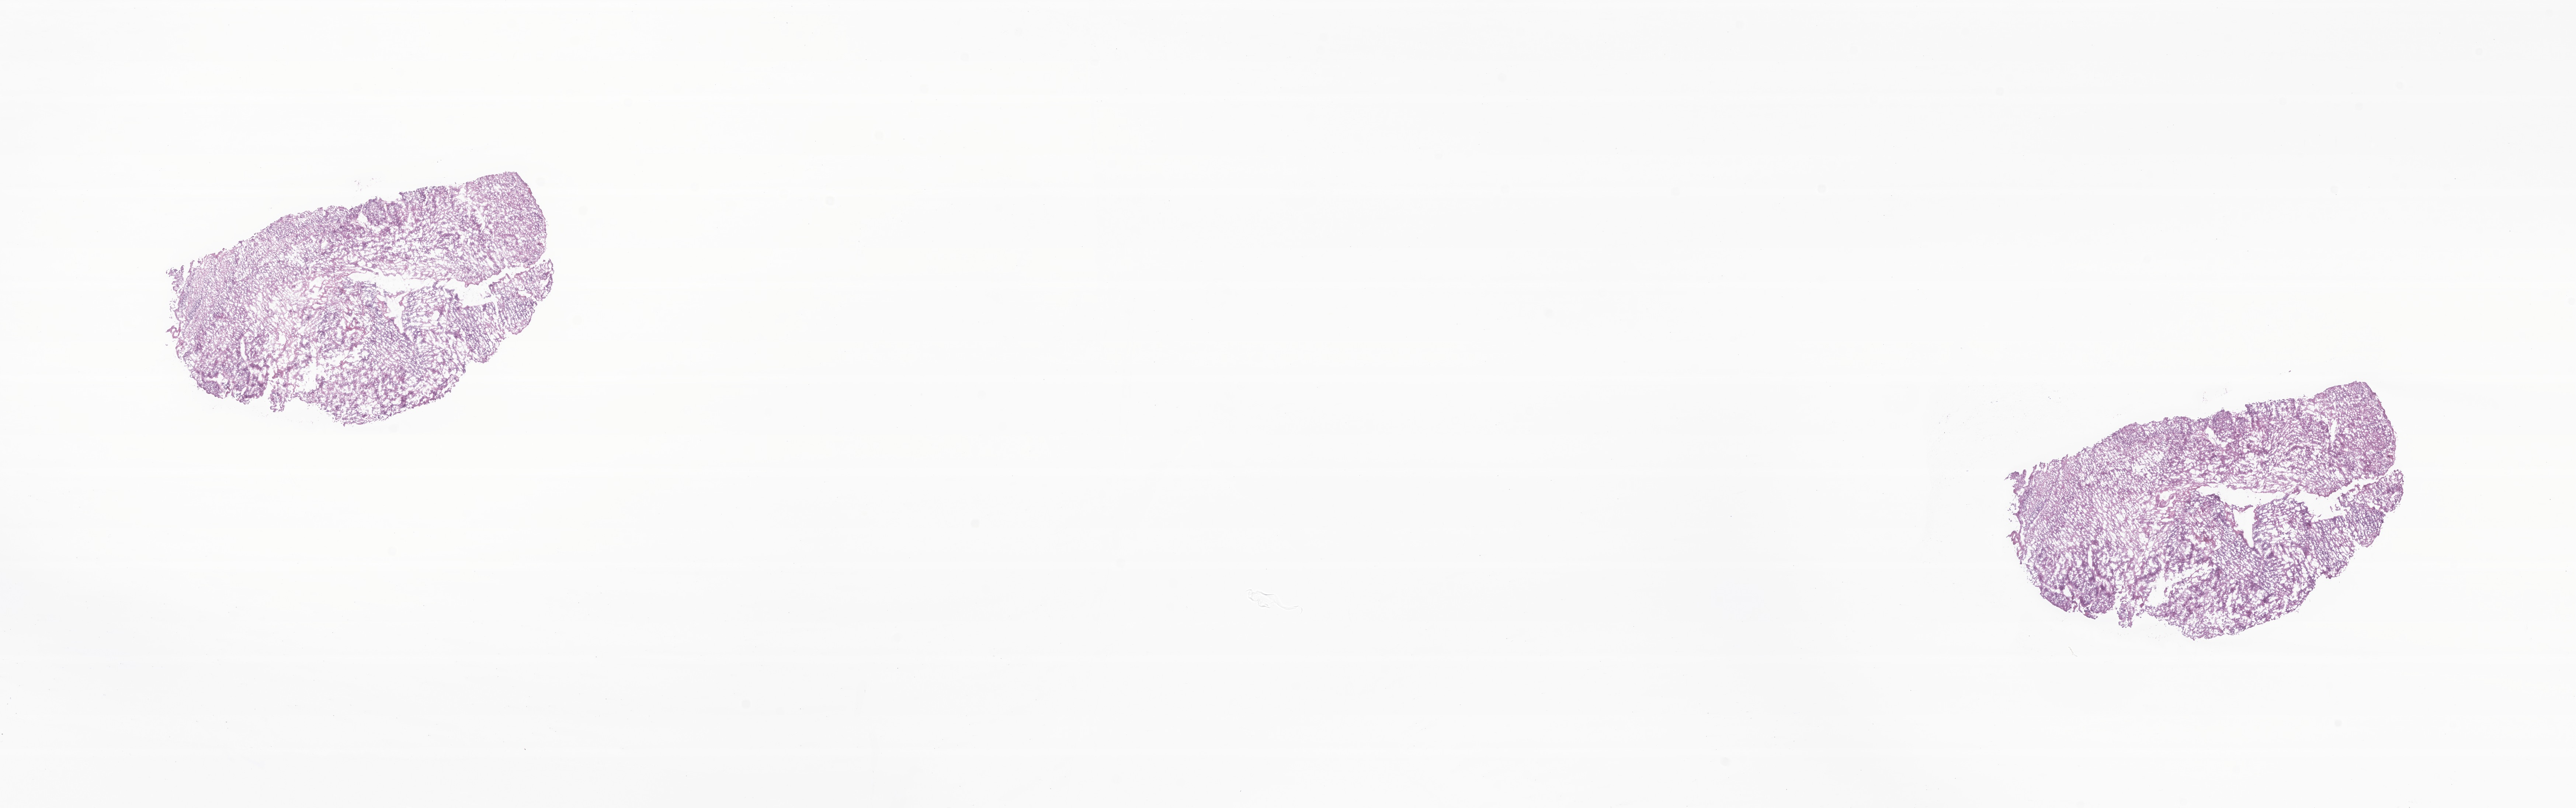
Digitized H&E-stained section of tumor tissue from the brain — a low-resolution overview of the entire scanned area, about 29.4 x 9.2 mm. Frozen section. Female patient, age 613 days (about 1.7 years).
Diagnosis (ICD-O-3 morphology term): Neoplasm, malignant.